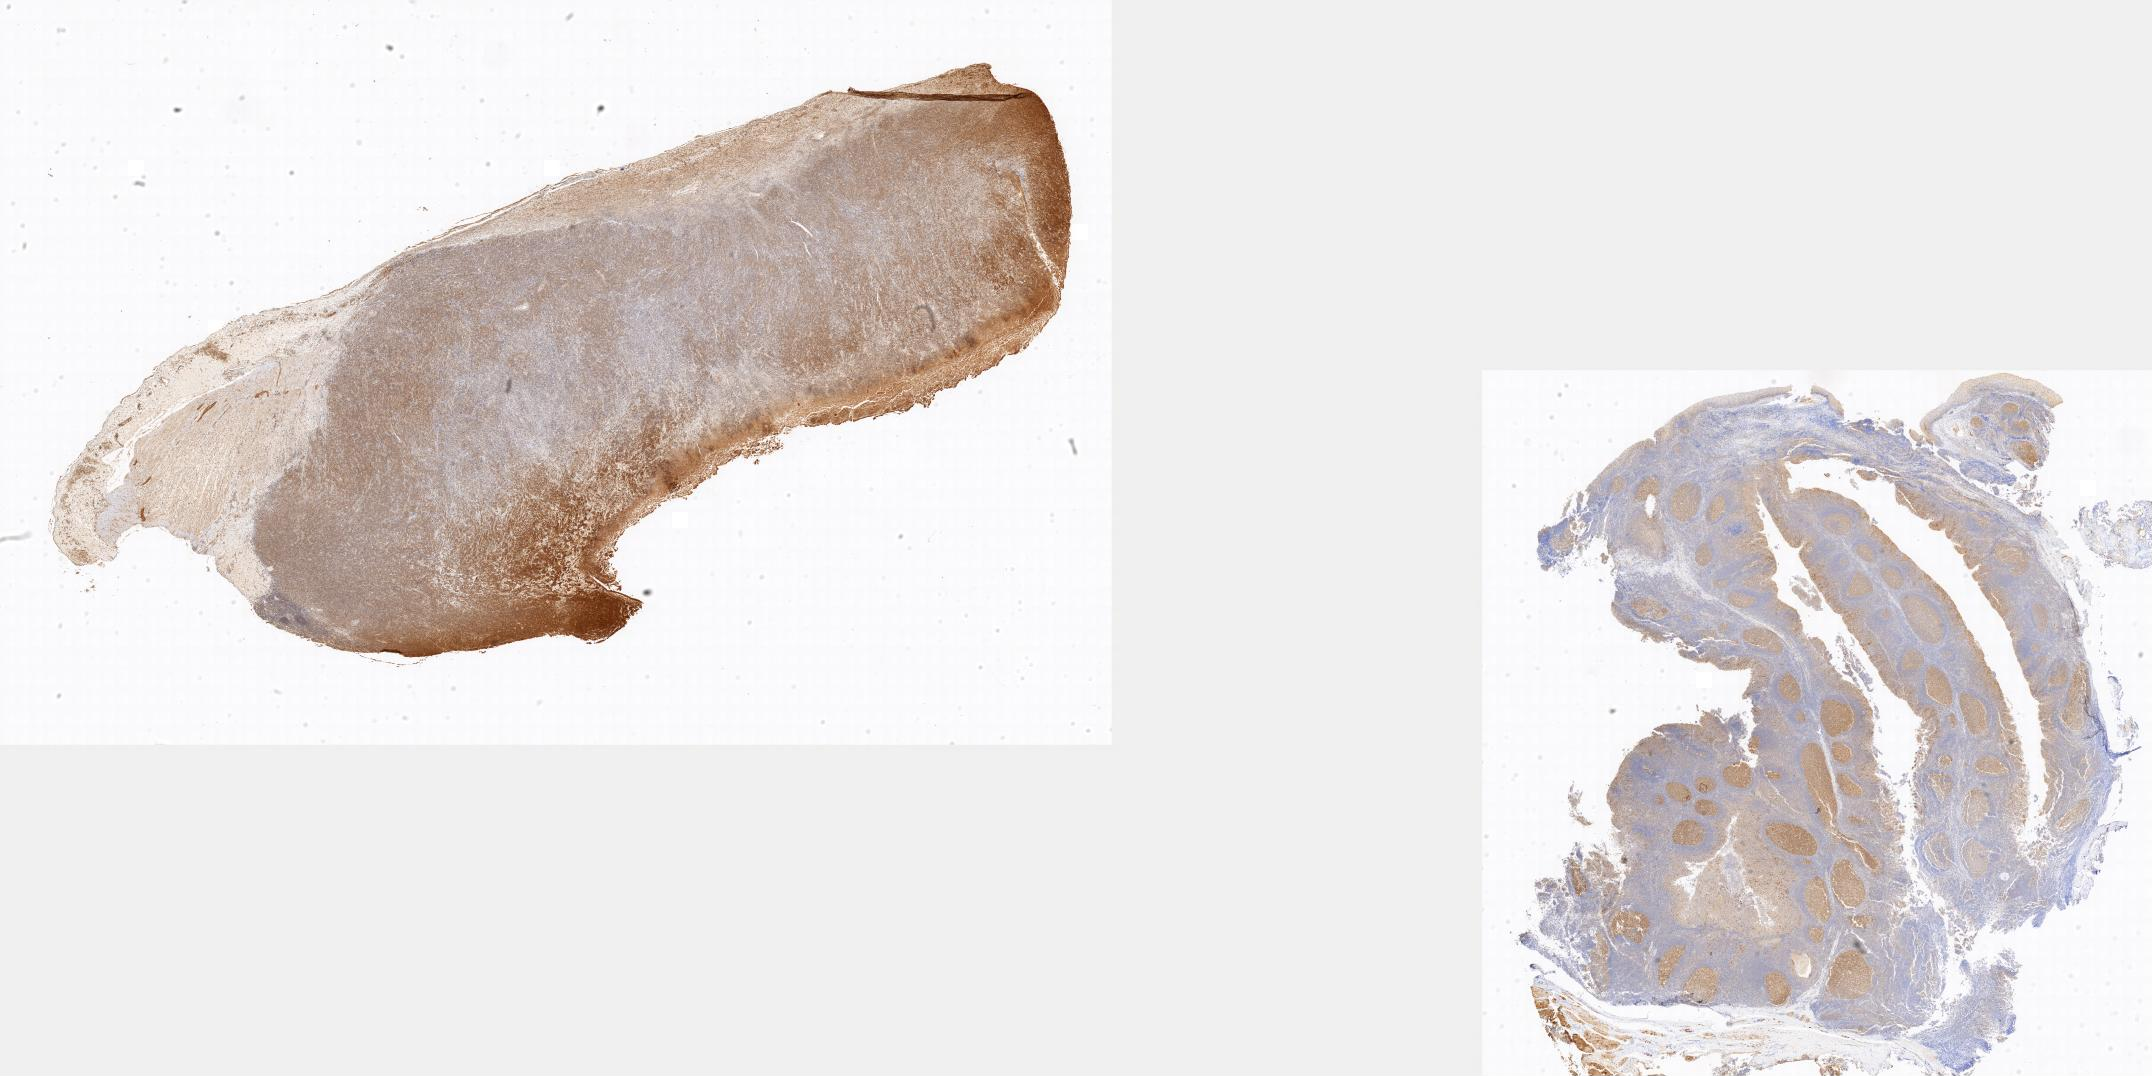
IHC for BCL6, whole-slide image, a low-resolution overview of the entire scanned area. Tumor tissue. Site: small intestine. Patient: male, age at initial diagnosis 3 years.
Diagnosis: Burkitt lymphoma, NOS.